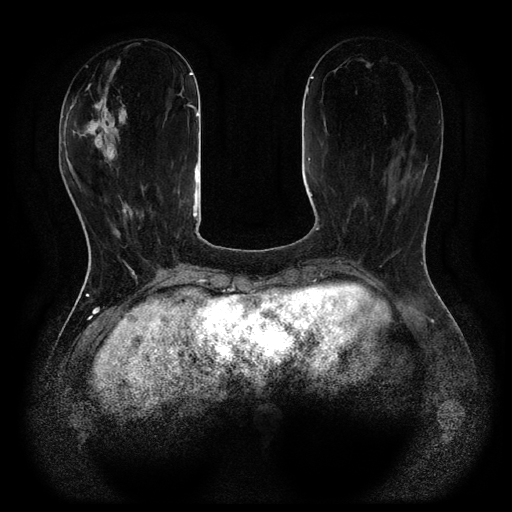
Breast MRI (dynamic contrast-enhanced, multi-phase), one axial slice. Position 33 of 116 along the scan axis. Dynamic contrast-enhanced series, time point 2 of 5 at this slice position (early post-contrast). 1.5 T. TE 2.6 ms, TR 5.4 ms. 512 × 512 image matrix. Patient: female, 48 years.
Structures marked on this image (semi-automatic segmentation, software-assisted and operator-edited):
- breast lesion (labelled benign in the annotation): box from (x=76, y=93) to (x=129, y=167) px